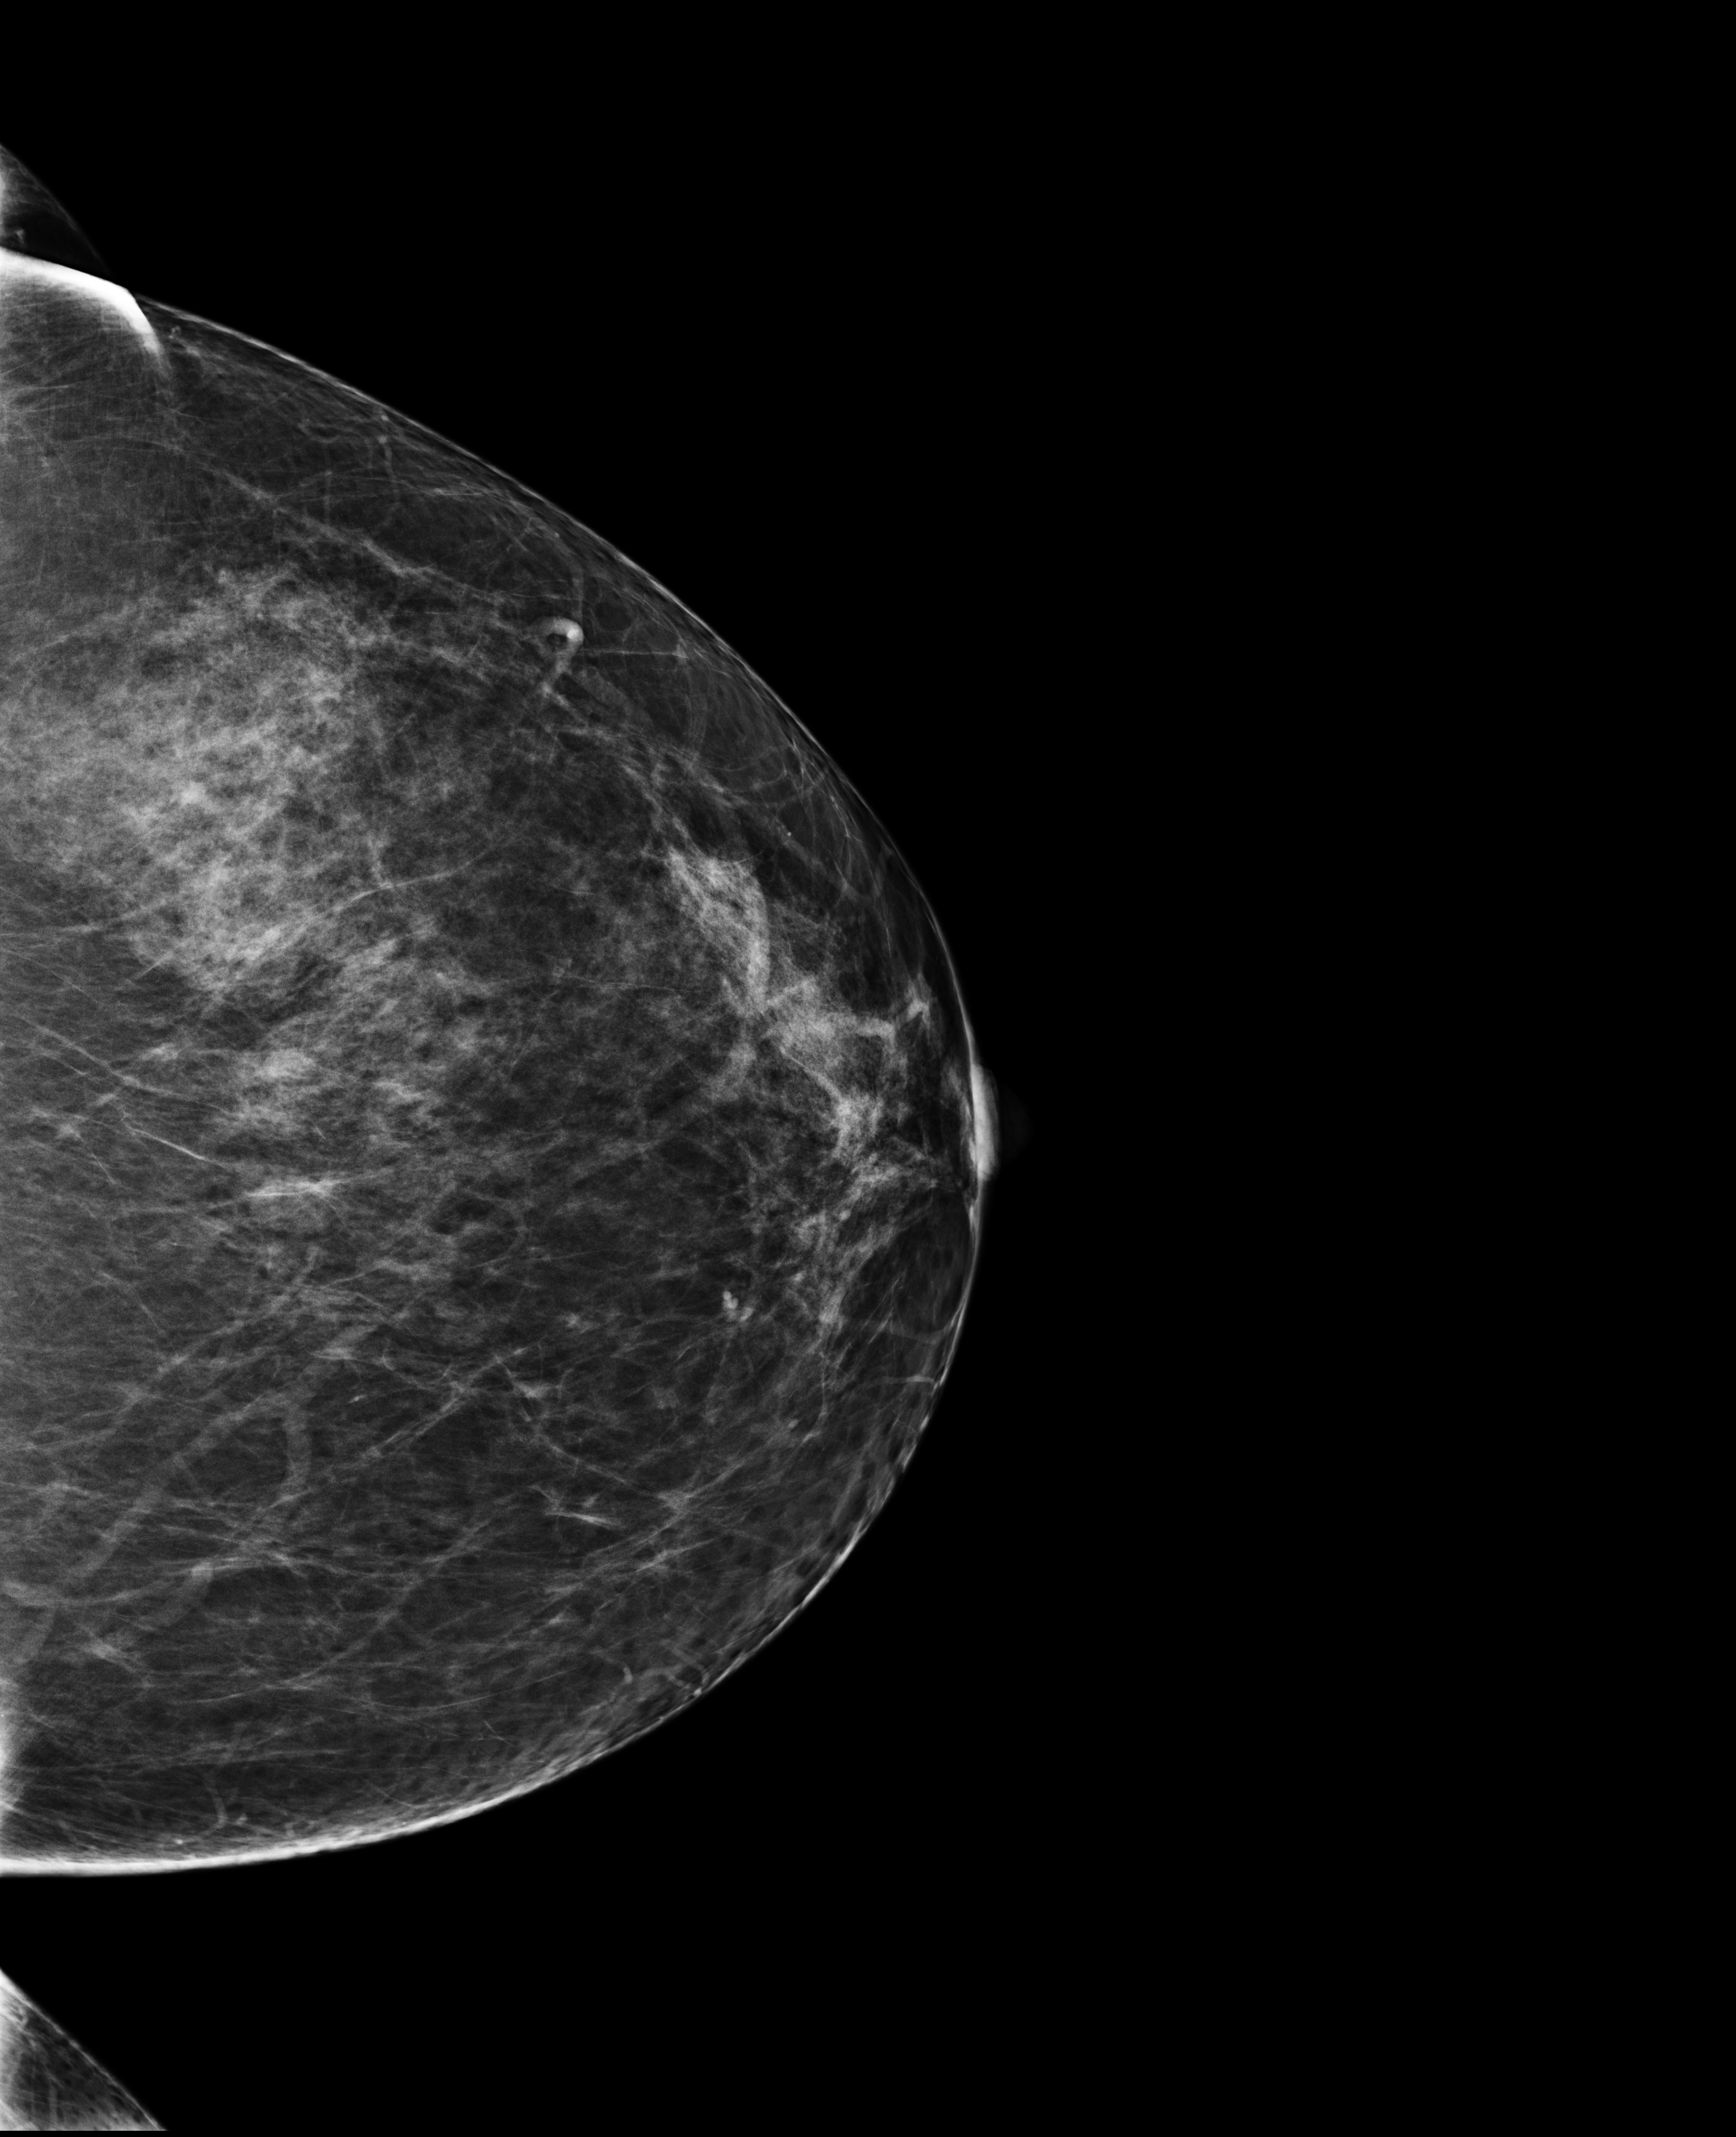
Annual screening mammography examination, system: Selenia Dimensions. Patient aged 48 years (female).
Image type: full-field digital mammogram. Breast: left. Projection: craniocaudal (CC) view.